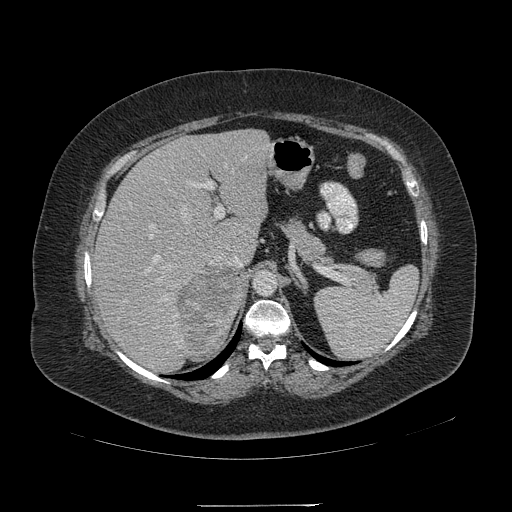
Contrast-enhanced abdominal CT, one axial slice. Slice 146 of 217 in the series (ordered by position). Reconstruction kernel STANDARD. Intravenous contrast given. Soft-tissue window (W 400 / L 40 HU). 512 × 512 image matrix. Female patient, age 55 years. From the clinical record (not read from this slice): diagnosis: adrenocortical carcinoma; tumour side: right adrenal; tumour size at pathology: 11 cm; Ki-67 index: 20 %; stage (as recorded): 2.
Structures marked on this image (semi-automatic segmentation, software-assisted and operator-edited):
- mass: bounding box (x1, y1, x2, y2) in pixels: (178, 266, 245, 354)